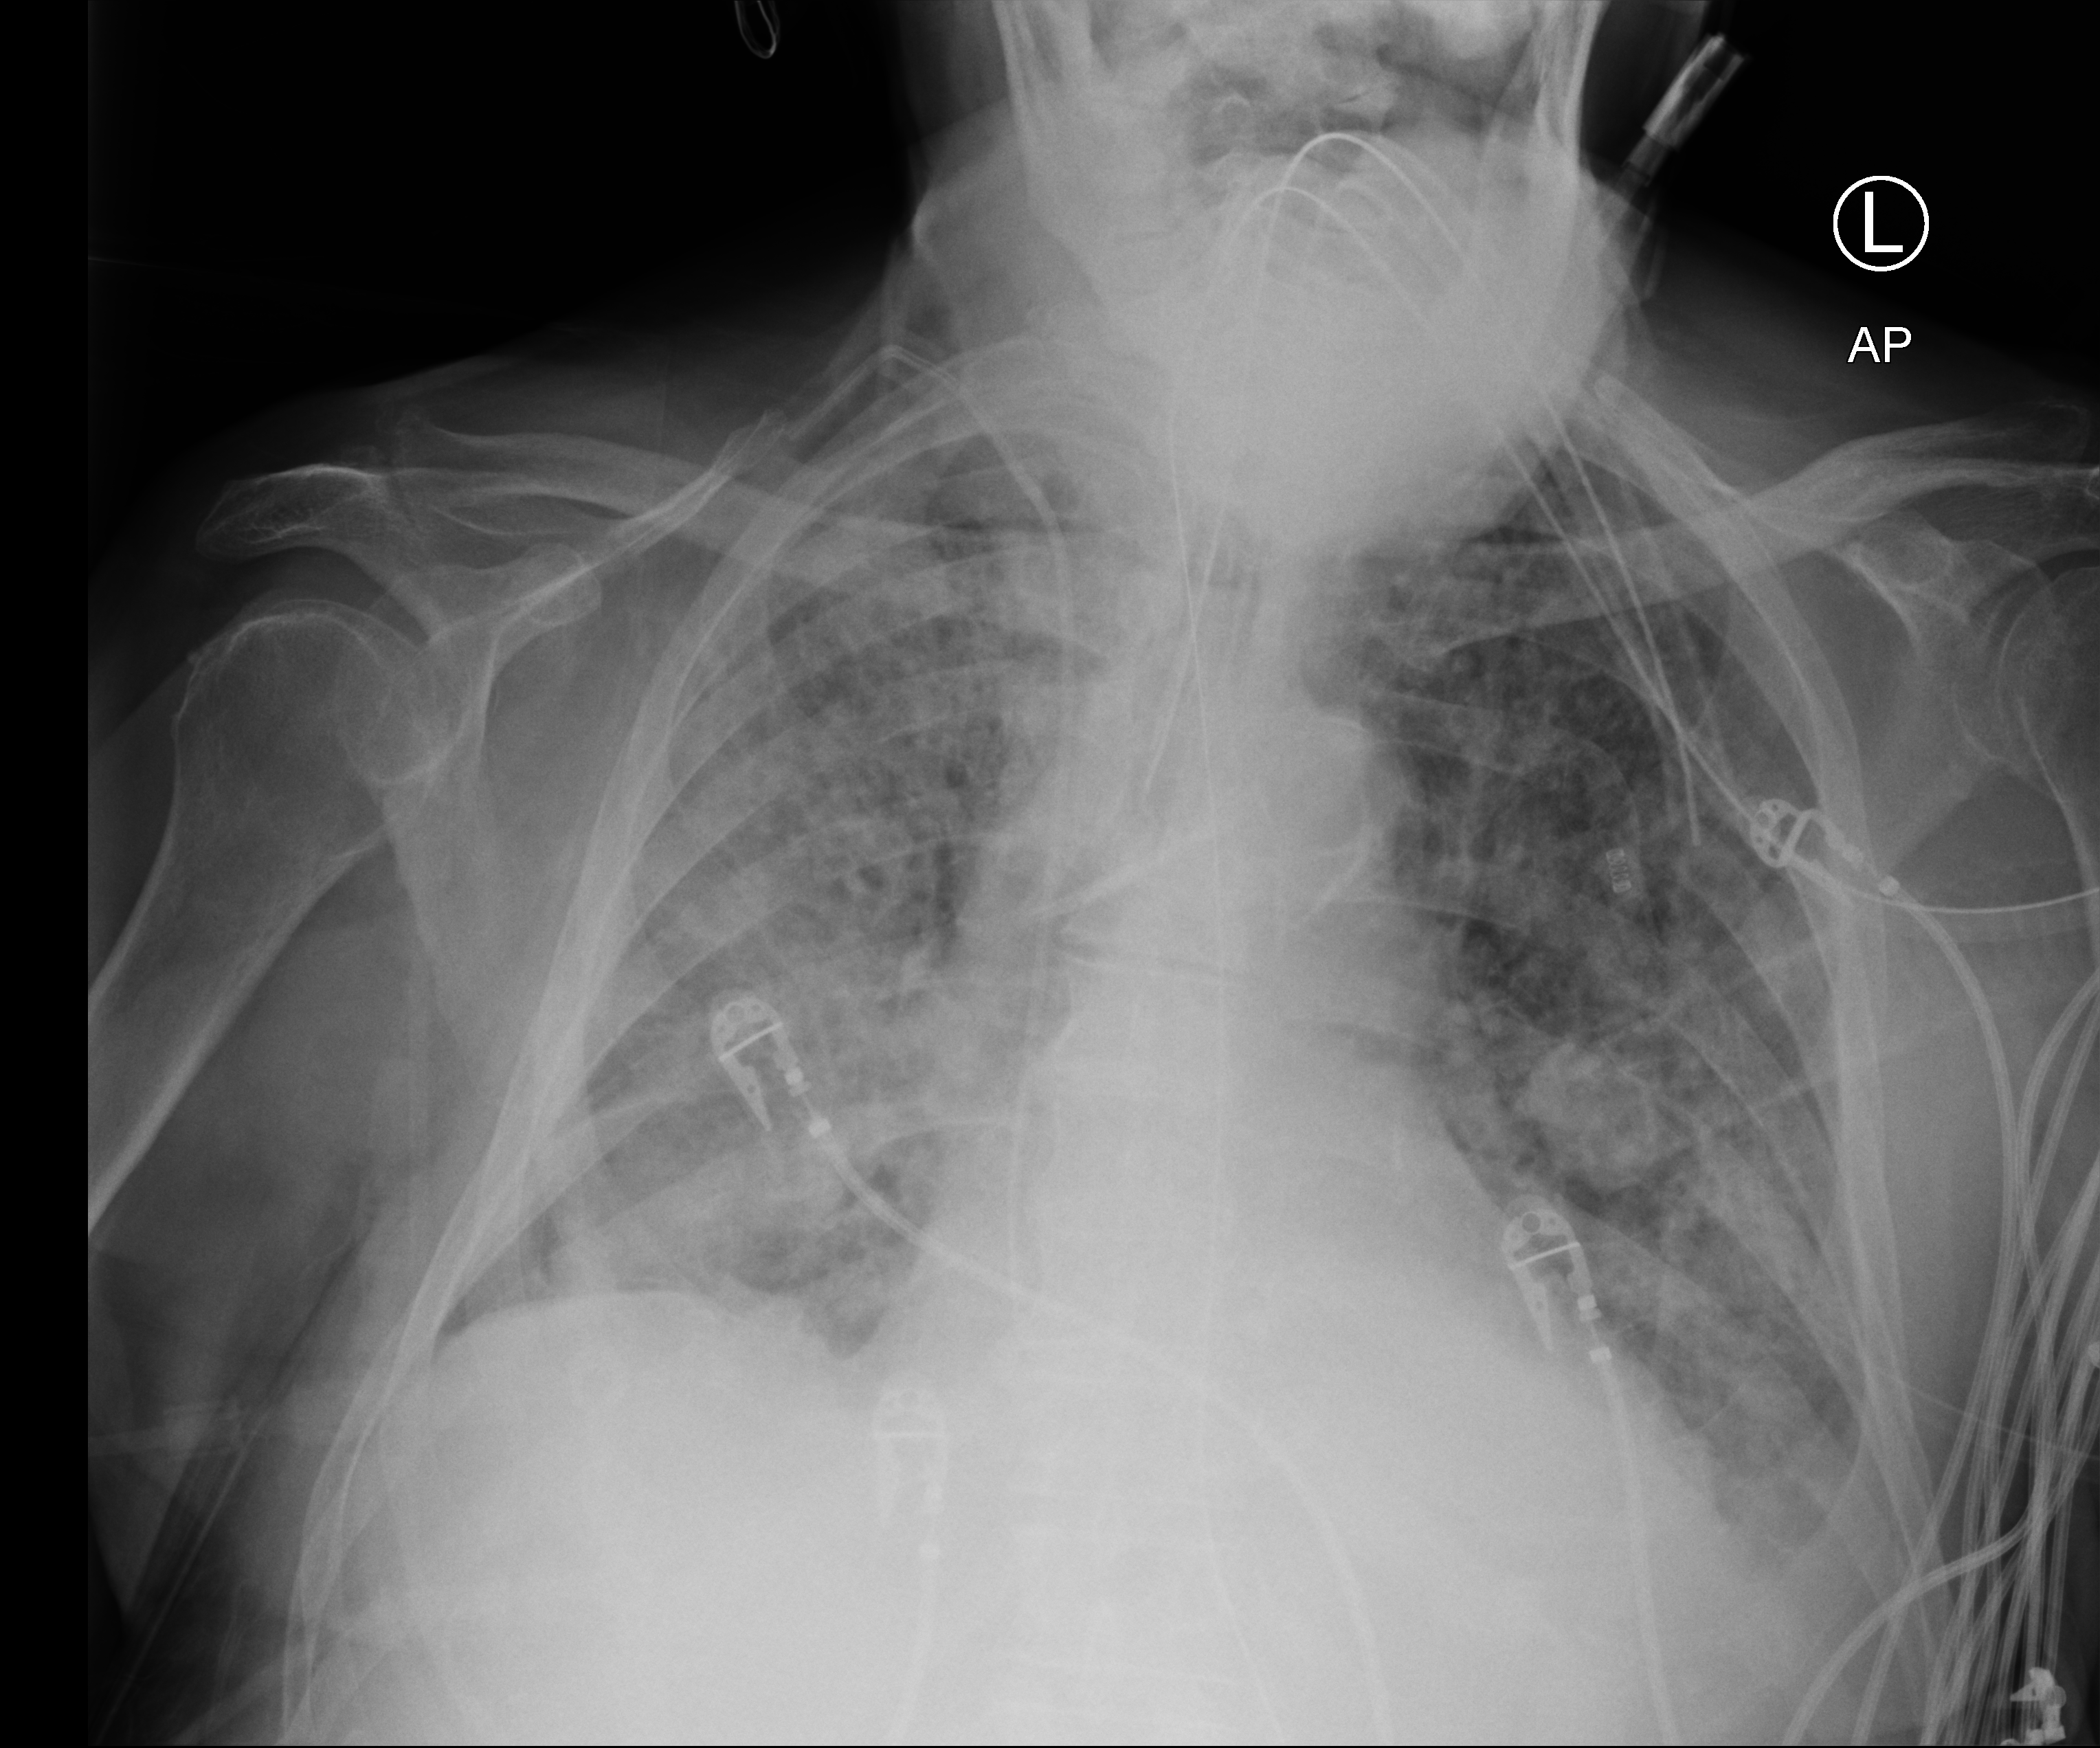
Portable chest radiograph; anteroposterior (AP) projection. Male patient hospitalised with COVID-19, age 75–90 years.
Admission-level facts for this patient (not findings on this image; timing relative to this image not recorded): mechanically ventilated during this hospital stay: yes; admitted to intensive care during this hospital stay: yes; length of hospital stay: 28 days.